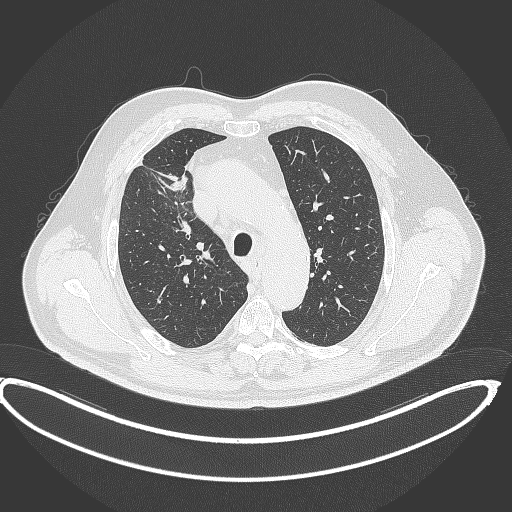
Chest CT, one axial slice; slice 304 of 390 in the series (ordered by position); reconstruction kernel B70f; lung window (W 1500 / L -600 HU); 1 mm slice thickness; 512 × 512 image matrix, field of view 448 × 448 mm. Male patient, age 62 years. From the clinical record (not read from this slice): clinical TNM (as recorded): T1c N3 M1c.
Annotated regions visible in this slice (rectangle marked by the reading radiologist):
- lung tumour (recorded histology: adenocarcinoma): bounding box [x1, y1, x2, y2] px = [166, 175, 192, 193]